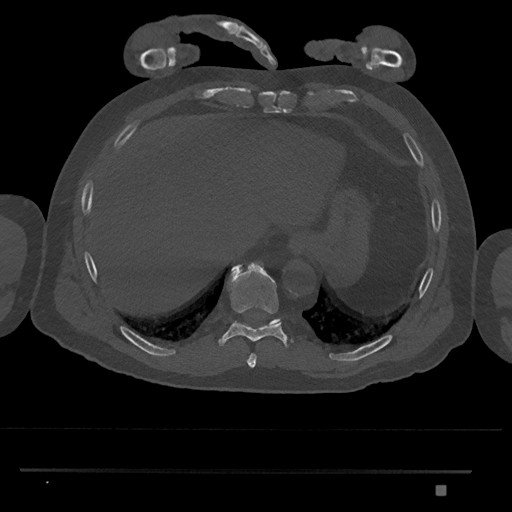
CT including the spine, one axial slice; position 1050 of 1134 along the scan axis; bone window (W 1800 / L 400 HU); 0.5 mm slice thickness; 512 × 512 image matrix, field of view 429 × 429 mm. Patient: male, 65 years. Case-level facts recorded for this patient, not image findings: primary cancer: prostate.
Structures marked on this image (semi-automatic segmentation, software-assisted and operator-edited):
- T10 vertebra: bounding box (x1, y1, x2, y2) in pixels: (234, 318, 281, 324)
- T8 vertebra: (247, 353, 257, 367)
- T9 vertebra: (219, 263, 287, 346)